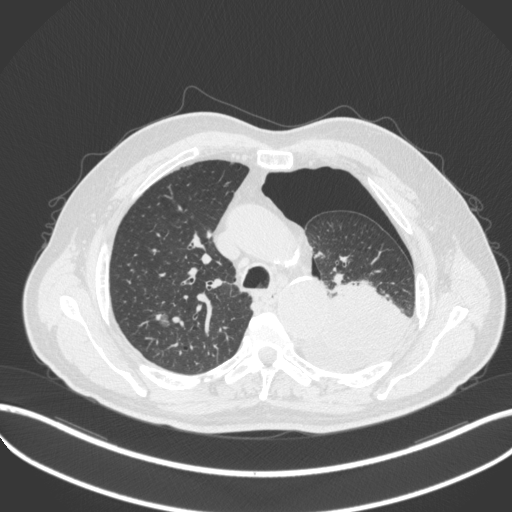
Chest CT, one axial slice; slice 364 of 466 in the series (ordered by position); reconstruction kernel B31f; lung window (W 1500 / L -600 HU); 1 mm slice thickness; 512 × 512 image matrix. Male patient, age 76 years. Case-level facts recorded for this patient, not image findings: clinical TNM (as recorded): T3 N0 M1b.
Outlined on this slice (bounding box drawn by a radiologist):
- lung tumour (recorded histology: adenocarcinoma): bounding box <297,282,413,371> (left, top, right, bottom; pixels)